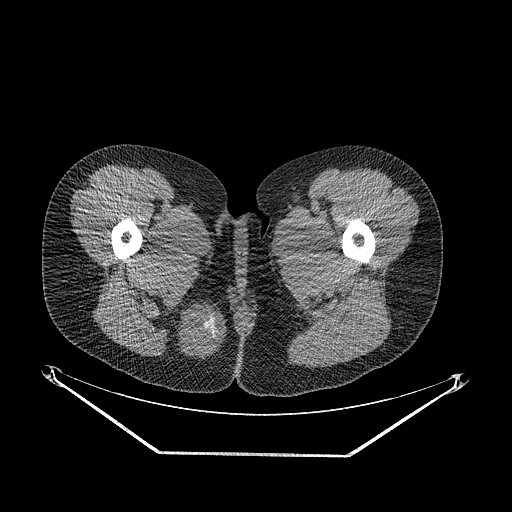
CT of an extremity soft-tissue mass (from a PET/CT study), one axial slice. Position 27 of 267 along the scan axis. Soft-tissue window (W 400 / L 40 HU). 3.75 mm slice thickness. 512 × 512 image matrix. Female patient. From the clinical record (not read from this slice): histological type: epithelioid sarcoma; grade: intermediate; site of the primary tumour: right buttock.
Annotated regions visible in this slice (expert contour drawn on MRI and transferred to this co-registered scan by the dataset authors):
- gross tumour volume including surrounding oedema: bounding box <173,299,225,359> (left, top, right, bottom; pixels)
- gross tumour volume (mass): <176,304,225,355>